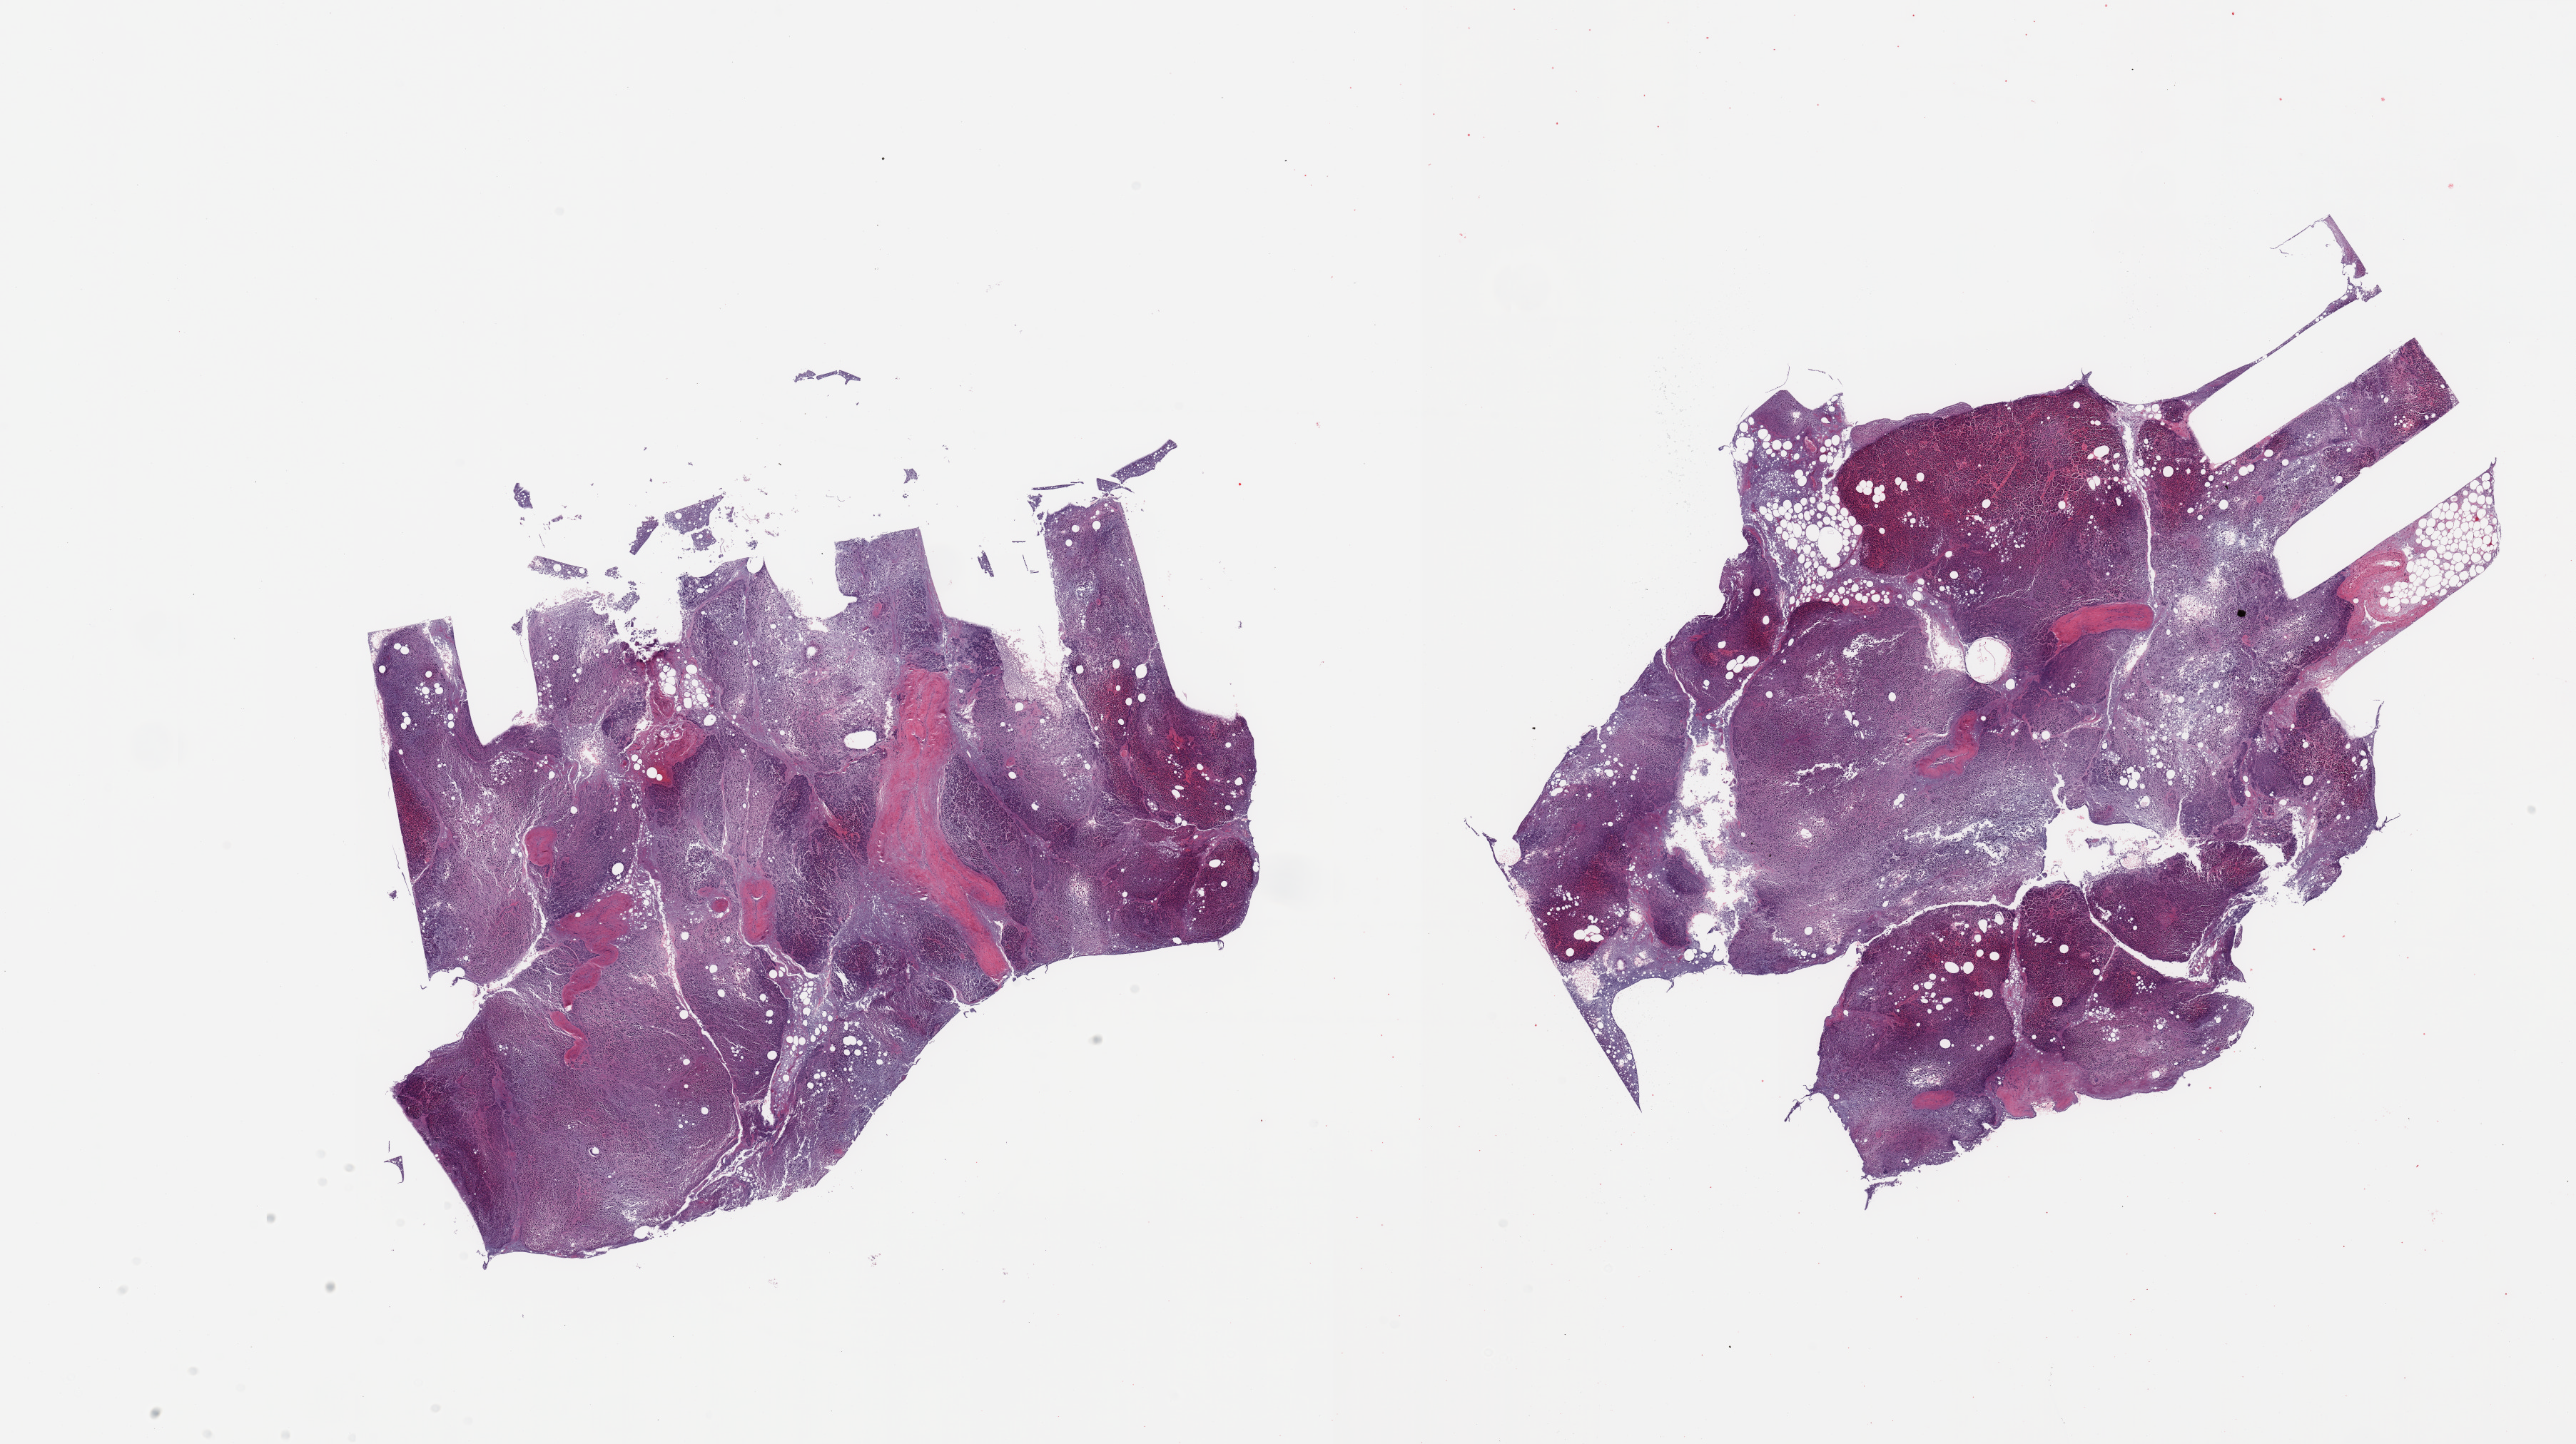
Digitized haematoxylin and eosin-stained section, shown as a low-resolution overview of the whole scanned area (about 28.5 x 16.0 mm, acquisition: 20x scan); PAXgene-fixed, paraffin-embedded tissue; target tissue: pancreas; donor tissue sample.
• pathologist's review note for this sample: 2 pieces; extensive autolysis